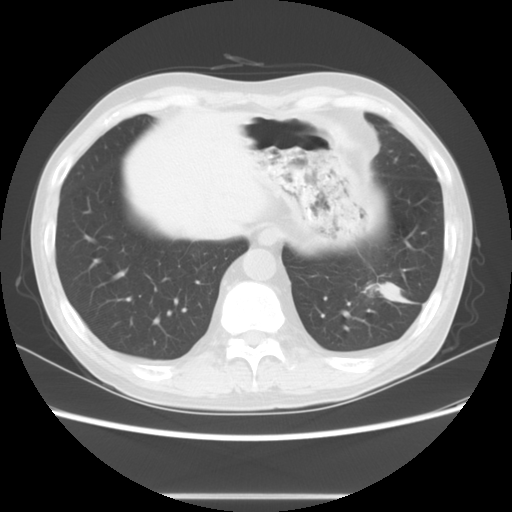
Chest CT, one axial slice; slice 20 of 63 in the series (ordered by position); reconstruction kernel STANDARD; 120 kVp; lung window (W 1500 / L -600 HU); 512 × 512 image matrix. Patient: male, 49 years. Case-level facts recorded for this patient, not image findings: clinical TNM (as recorded): T3 N0 M0; histopathological grade: G2-3.
Structures marked on this image (bounding box drawn by a radiologist):
- lung tumour (recorded histology: squamous cell carcinoma): box from (x=366, y=270) to (x=411, y=312) px